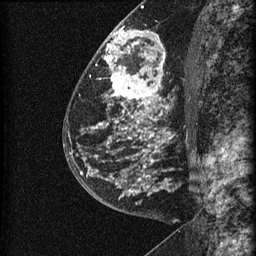
Breast MRI (dynamic contrast-enhanced), one sagittal slice; dynamic contrast-enhanced series, image 2 of 3 at this slice position (ordered by acquisition); 1.5 T; TE 4.2 ms, TR 22.7 ms; 1.5 mm slice thickness; 256 × 256 image matrix, field of view 180 × 180 mm. Female patient, age 48 years. From the clinical record (not read from this slice): setting: breast cancer imaged before/during neoadjuvant chemotherapy; receptor status: triple-negative.
Annotated regions visible in this slice (semi-automatically segmented with operator editing):
- analysis volume of interest (the breast-tissue region the enhancement analysis was run in; not a lesion): bounding box [x1, y1, x2, y2] px = [81, 23, 186, 202]
- tumour enhancement mask (voxels above the 90 % enhancement threshold inside the analysis volume of interest): [81, 30, 164, 197]